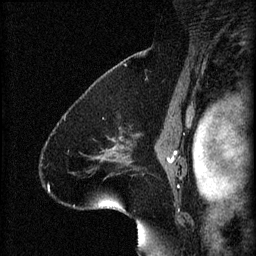
Breast MRI (dynamic contrast-enhanced), one sagittal slice; position 46 of 60 along the scan axis; 3 images stored at this slice position (order not interpretable as contrast timing); 1.5 T; TE 4.2 ms, TR 8.2 ms; 2 mm slice thickness; 256 × 256 image matrix, field of view 180 × 180 mm. Patient: female, 41 years.
Outlined on this slice (semi-automatically segmented with operator editing):
- analysis volume of interest (the breast-tissue region the enhancement analysis was run in; not a lesion): bounding box <76,130,134,195> (left, top, right, bottom; pixels)
- tumour enhancement mask (voxels above the 70 % enhancement threshold inside the analysis volume of interest): <109,150,111,155>